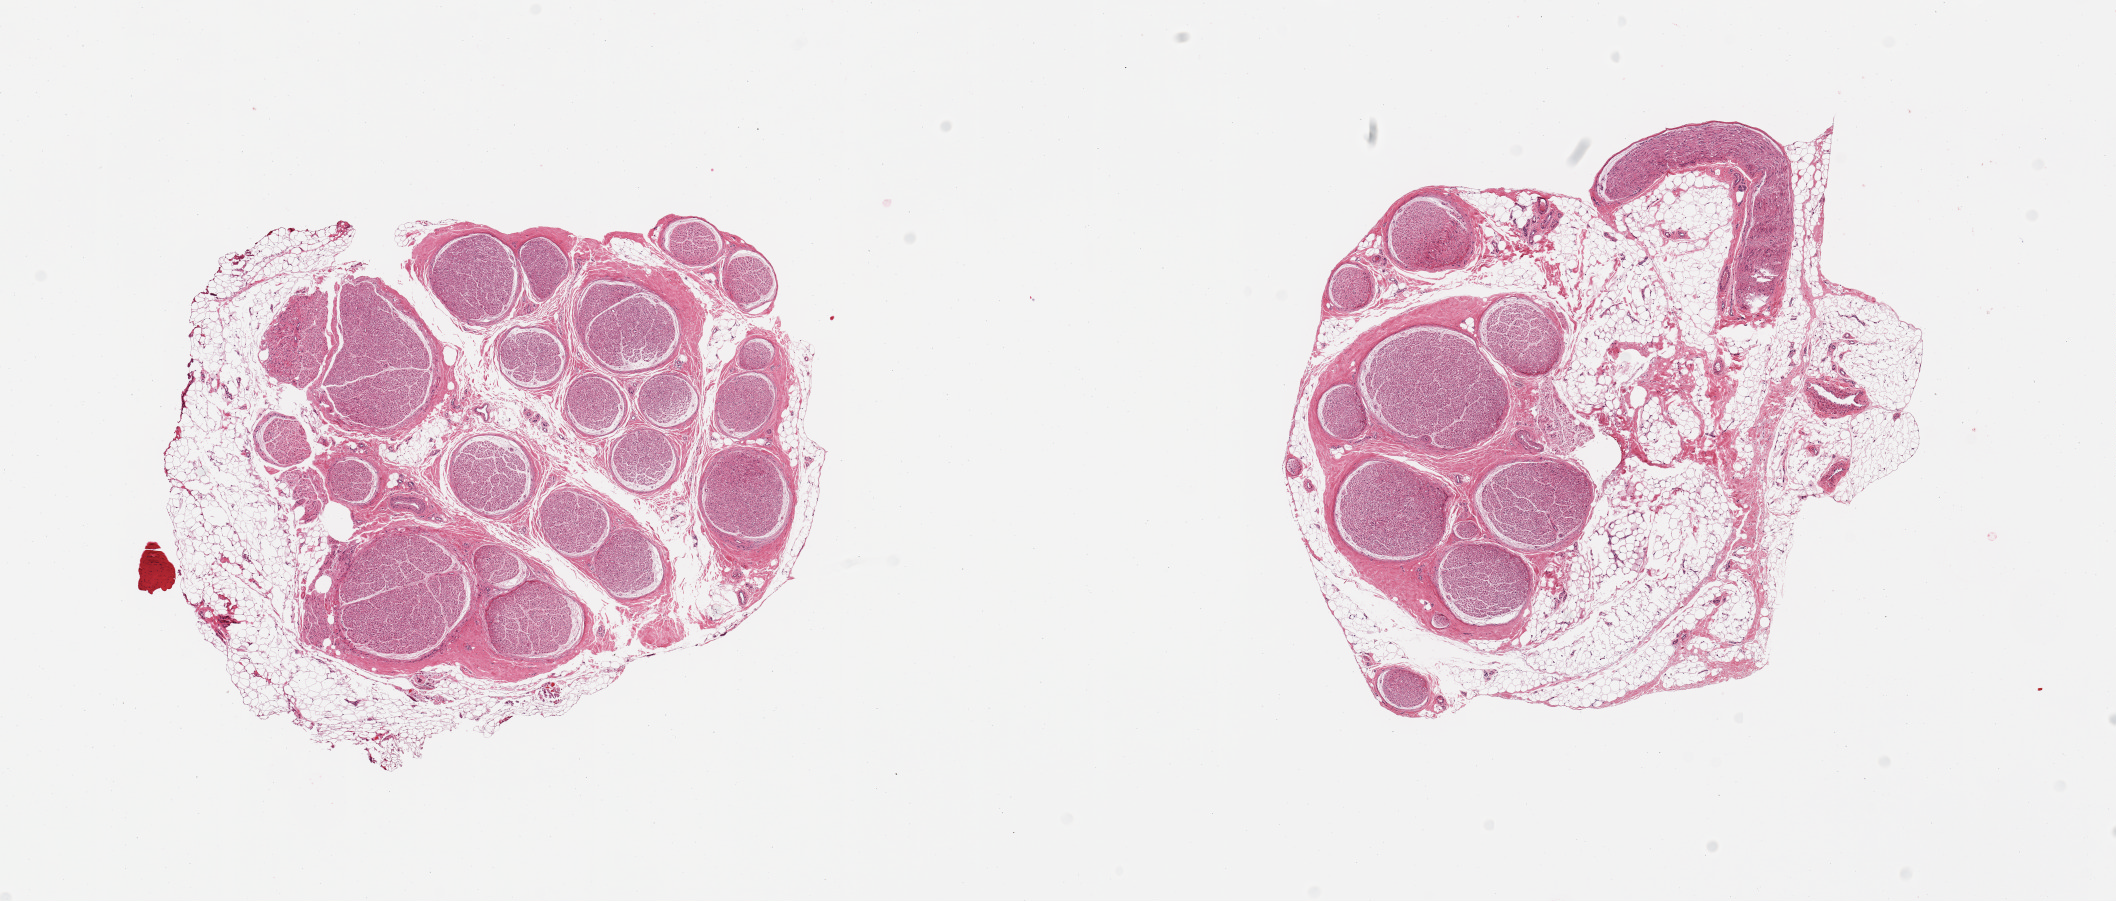
Whole-slide image, haematoxylin and eosin stain — shown as a low-resolution overview of the whole scanned area (about 16.7 x 7.1 mm), PAXgene-fixed, paraffin-embedded tissue, target tissue: tibial nerve, tissue donor sample.
Review note (as recorded): 2 pieces, partial rims of adherent fat up to ~2mm.